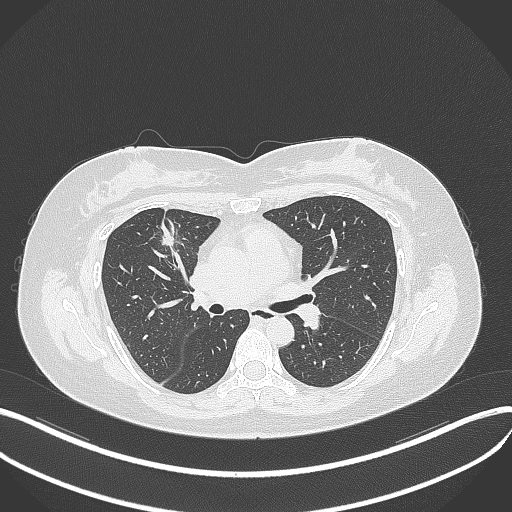
Chest CT, one axial slice. Position 188 of 273 along the scan axis. Reconstruction kernel B70f. Lung window (W 1500 / L -600 HU). 1 mm slice thickness. 512 × 512 image matrix, field of view 400 × 400 mm. Patient: female, 42 years. From the clinical record (not read from this slice): clinical TNM (as recorded): T1b N0 M0.
Outlined on this slice (rectangle marked by the reading radiologist):
- lung tumour (recorded histology: adenocarcinoma): bounding box (x1, y1, x2, y2) in pixels: (157, 223, 180, 251)